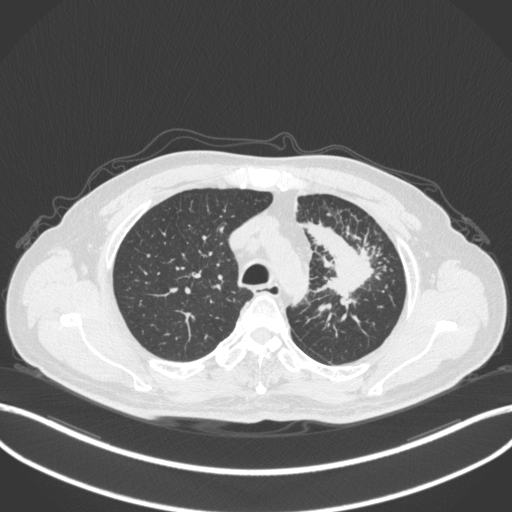
Chest CT, one axial slice; slice 273 of 386 in the series (ordered by position); reconstruction kernel B31f; lung window (W 1500 / L -600 HU); 1 mm slice thickness; 512 × 512 image matrix, field of view 400 × 400 mm. Patient: male, 69 years. From the clinical record (not read from this slice): clinical TNM (as recorded): T2a N2 M0.
Structures marked on this image (rectangle marked by the reading radiologist):
- lung tumour (recorded histology: adenocarcinoma): box from (x=302, y=221) to (x=375, y=295) px